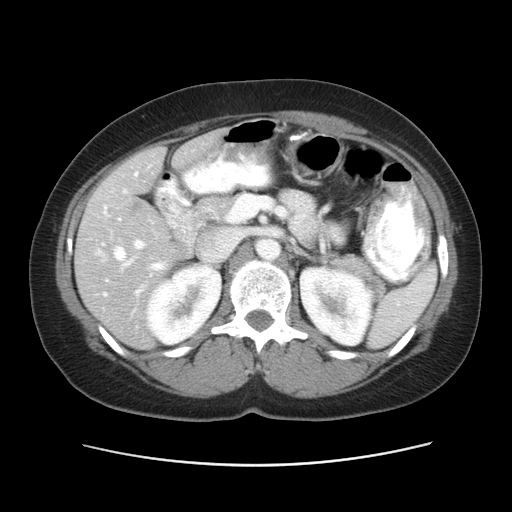
Contrast-enhanced abdominal CT, one axial slice; slice 29 of 52 in the series (ordered by position); reconstruction kernel STANDARD; soft-tissue window (W 400 / L 40 HU); 5 mm slice thickness; 512 × 512 image matrix, field of view 362 × 362 mm. Female patient, age 48 years. Case-level facts recorded for this patient, not image findings: diagnosis: colorectal cancer liver metastases, imaged before liver resection; multiple liver metastases: yes; largest metastasis: 4.5 cm; disease in both lobes: yes.
Annotated regions visible in this slice (expert manual segmentation):
- hepatic veins: bounding box <97,218,165,296> (left, top, right, bottom; pixels)
- liver: <76,133,220,349>
- planned liver remnant (the part of the liver to remain after resection): <176,133,220,166>
- portal vein (with intrahepatic branches): <123,172,145,249>
- liver metastasis: <132,204,139,214>